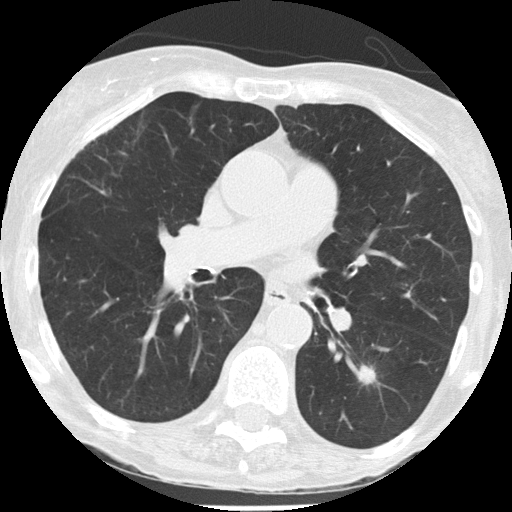
Low-dose screening chest CT, one axial slice. Slice 71 of 146 in the series (ordered by position). Reconstruction kernel FC51. Lung window (W 1500 / L -600 HU). 2 mm slice thickness. 512 × 512 image matrix.
Outlined on this slice (manually delineated by an expert):
- lesion 1 (tumor, lower lobe of left lung): bounding box [x1, y1, x2, y2] px = [358, 365, 376, 384]